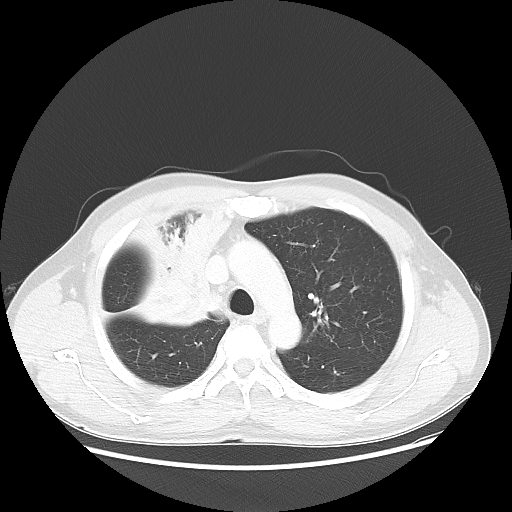
Chest CT, one axial slice; slice 39 of 56 in the series (ordered by position); 100 kVp; lung window (W 1500 / L -600 HU); 5 mm slice thickness; 512 × 512 image matrix, field of view 398 × 398 mm. Patient: male, 60 years. Case-level facts recorded for this patient, not image findings: clinical TNM (as recorded): T2a N1 M0.
Structures marked on this image (rectangle marked by the reading radiologist):
- lung tumour (recorded histology: squamous cell carcinoma): bounding box (x1, y1, x2, y2) in pixels: (107, 205, 224, 326)